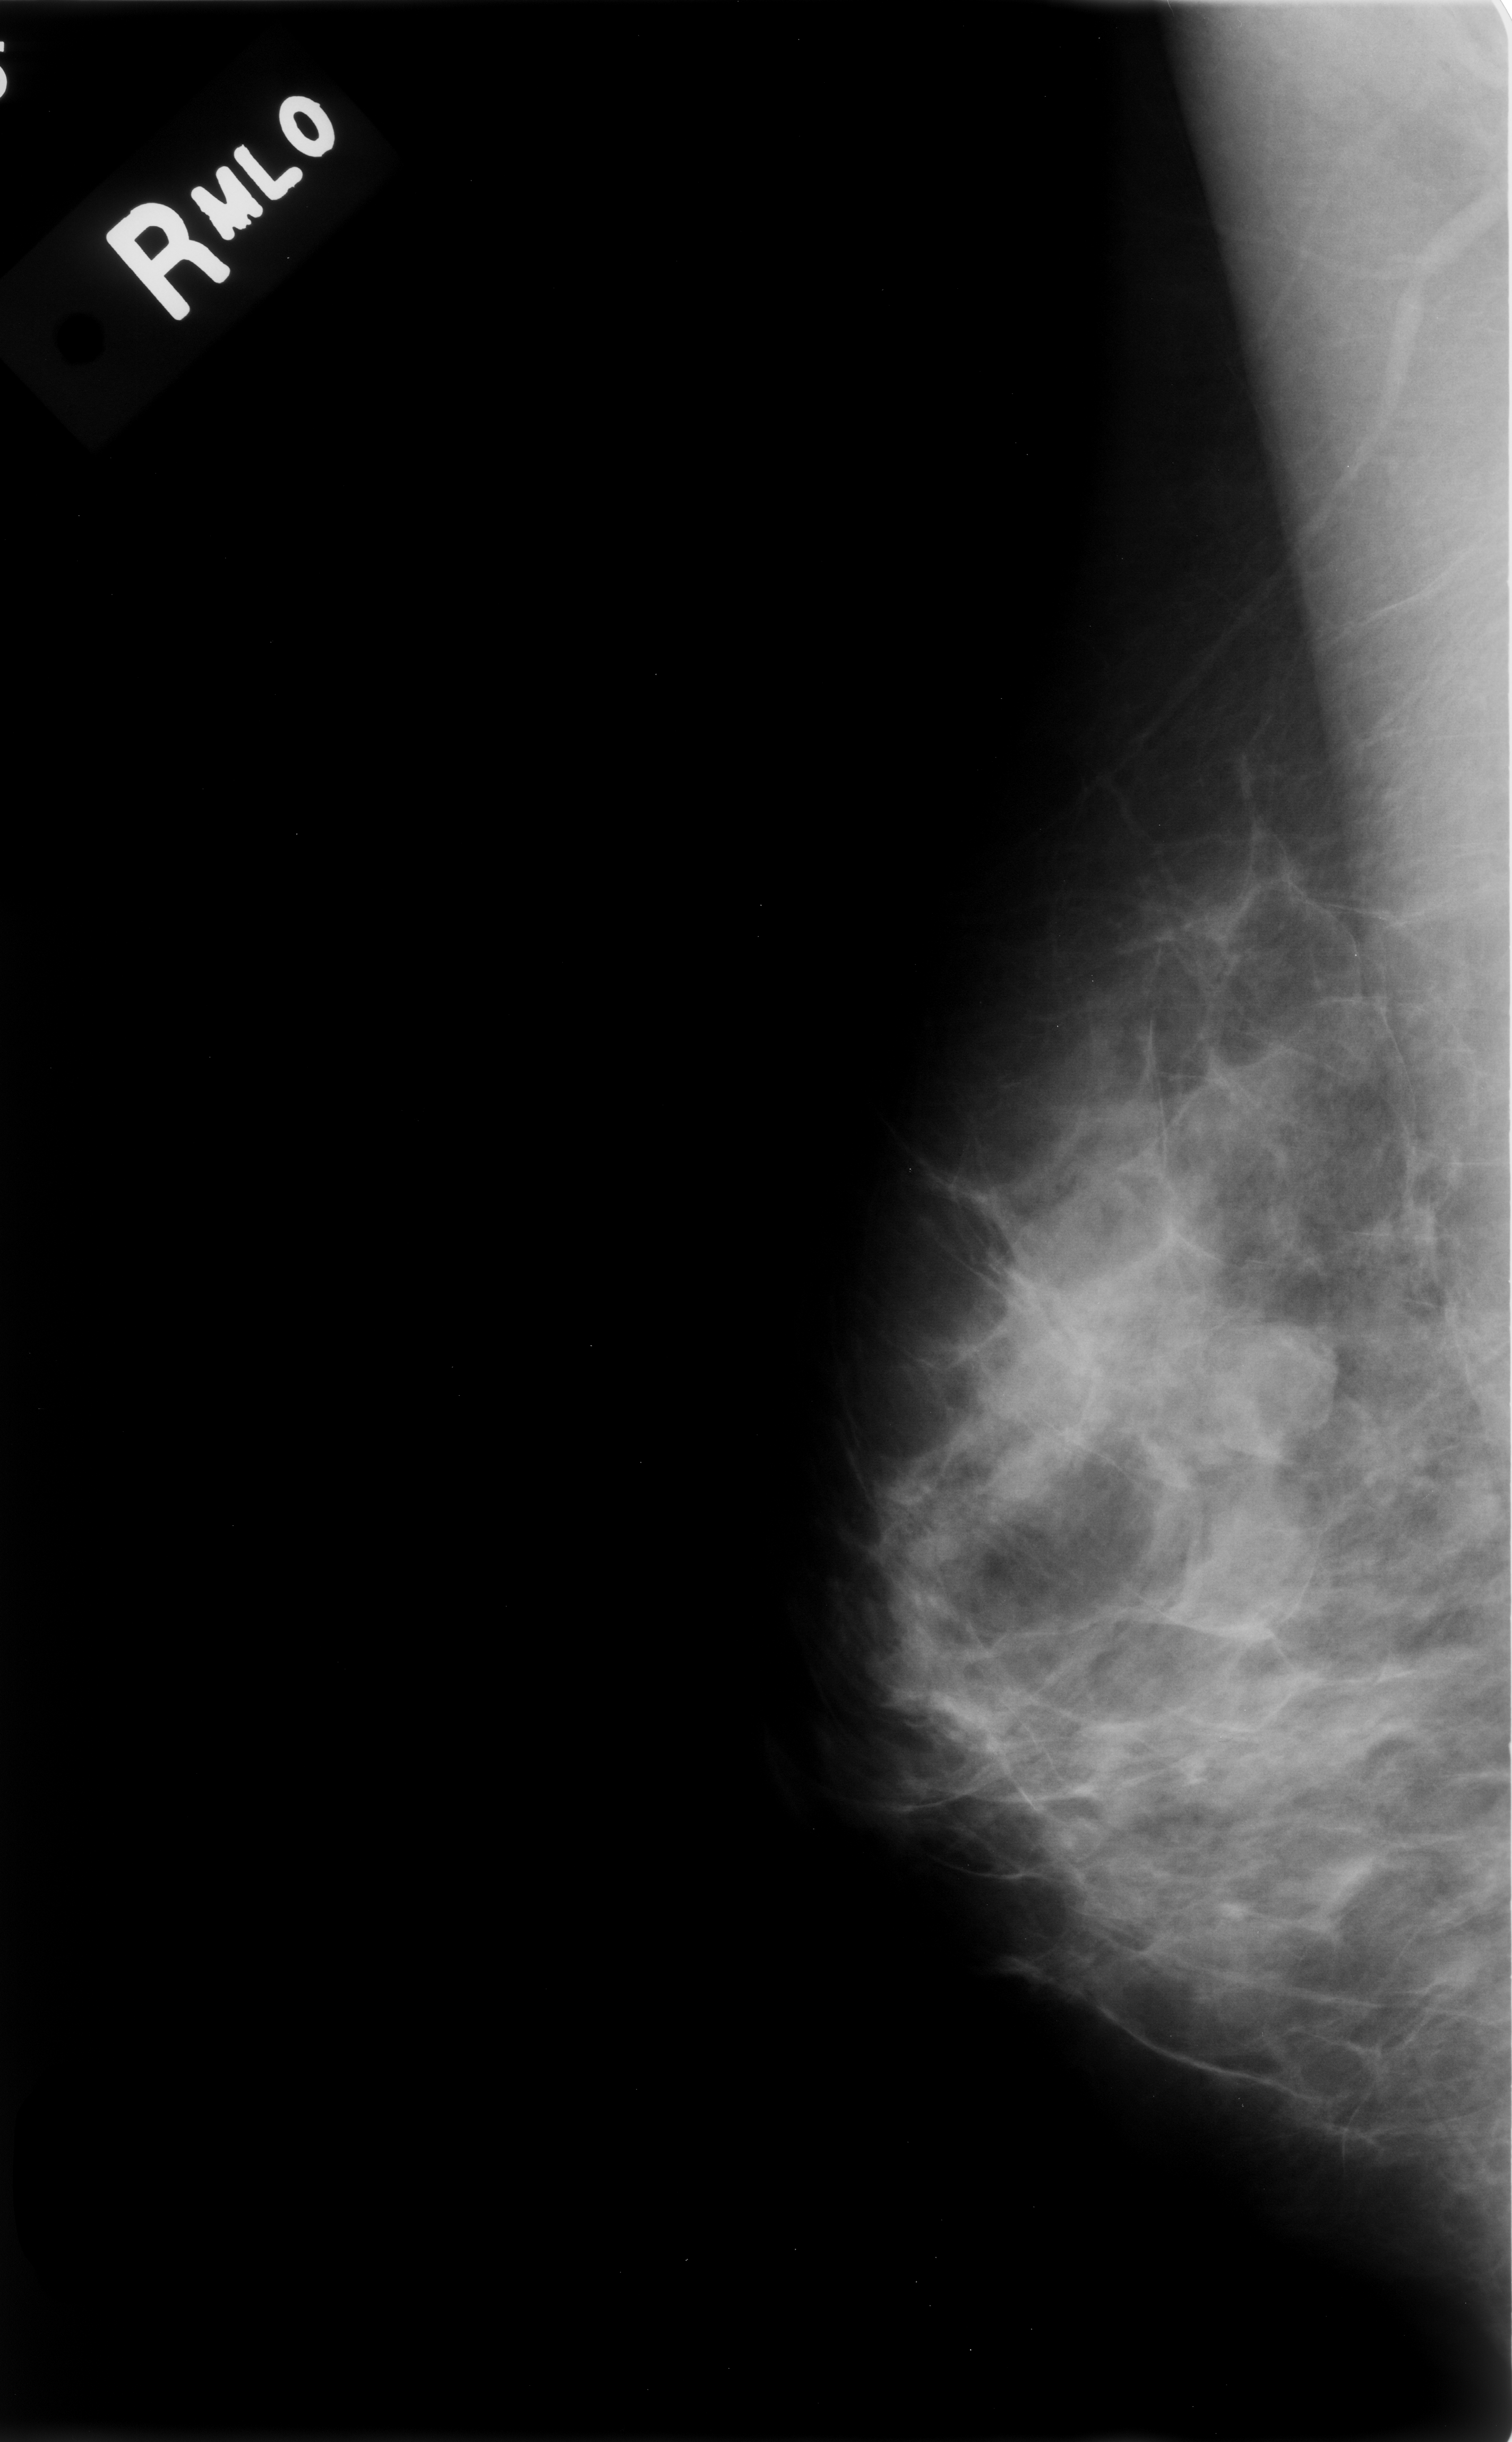
Digitized screen-film mammogram; right breast; mediolateral oblique (MLO) view; BI-RADS breast density category 2 (scale 1–4); 1512 × 2442 image matrix.
Marked abnormalities (boxes around the expert regions of interest):
- mass, shape round, margins circumscribed; BI-RADS assessment category 3; subtlety rating 3 on a 1 (subtle) to 5 (obvious) scale; pathology (as recorded): benign: bounding box (x1, y1, x2, y2) in pixels: (1204, 1309, 1340, 1478)